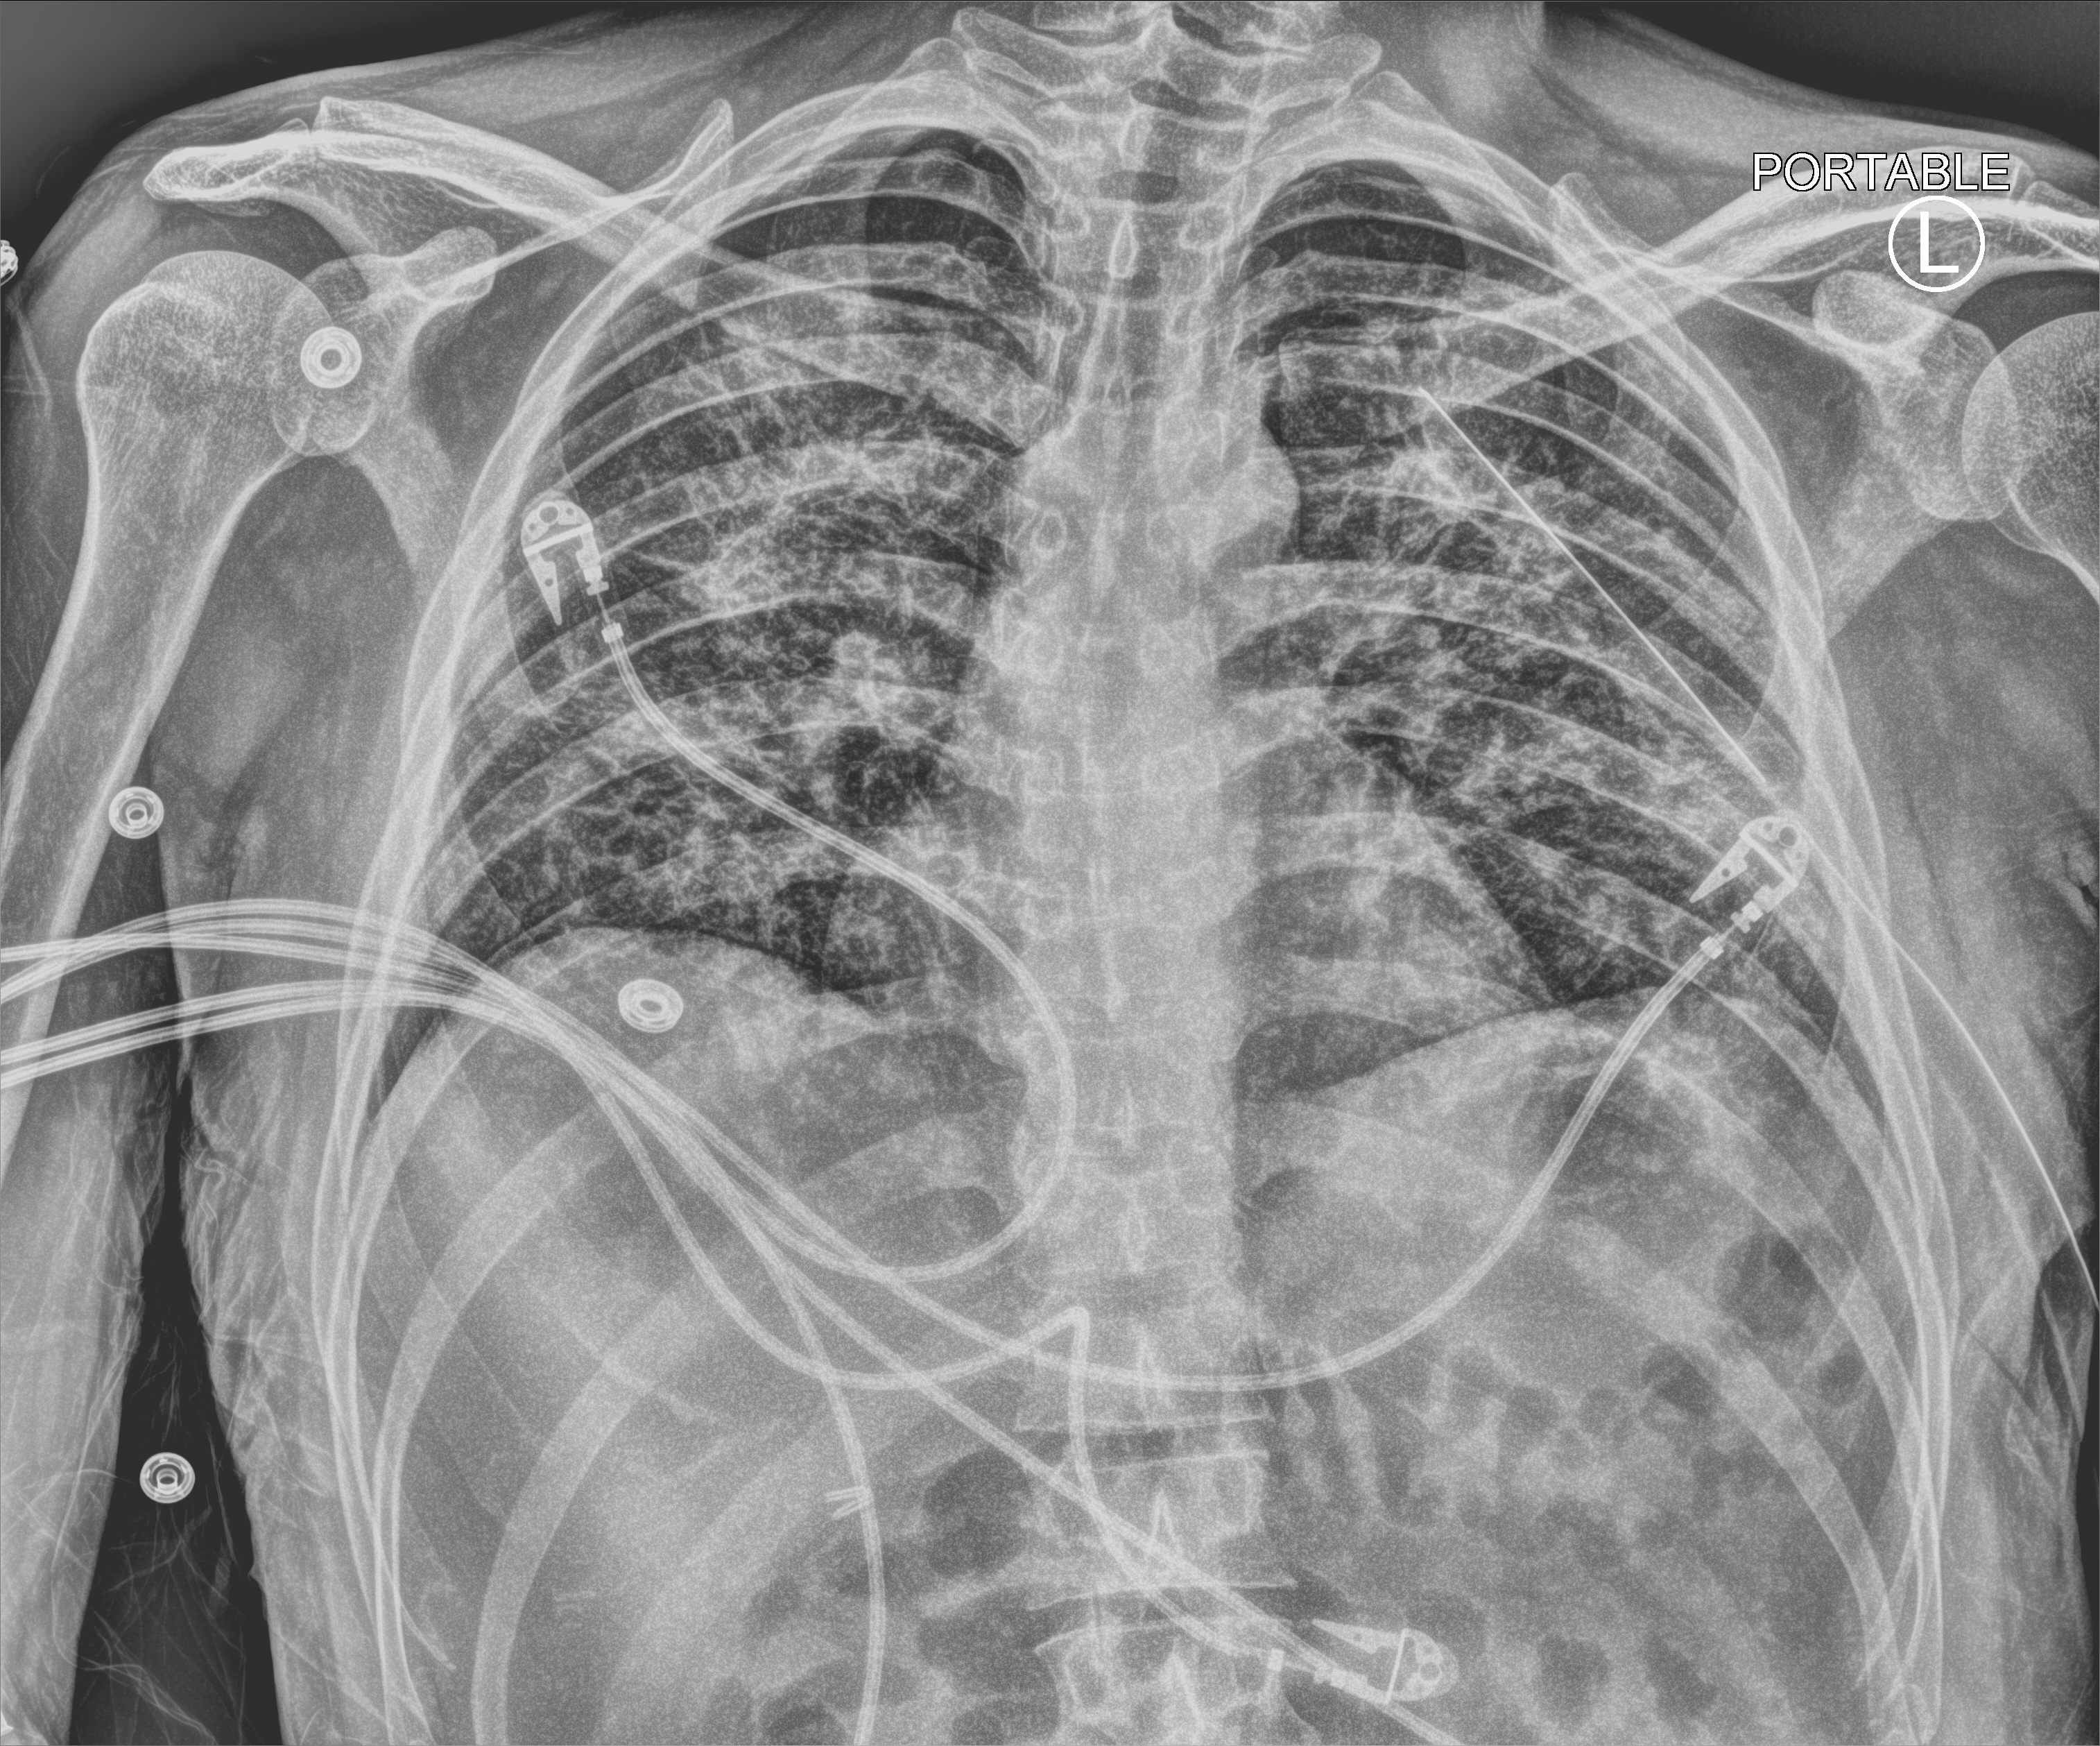
Portable chest radiograph; anteroposterior (AP) projection. Patient hospitalised with COVID-19; male, aged 18–59 years.
From the hospital-stay record, not from the radiograph (when in the stay this image was taken is not recorded):
- diabetes (admission record): no
- chronic kidney disease (admission record): no